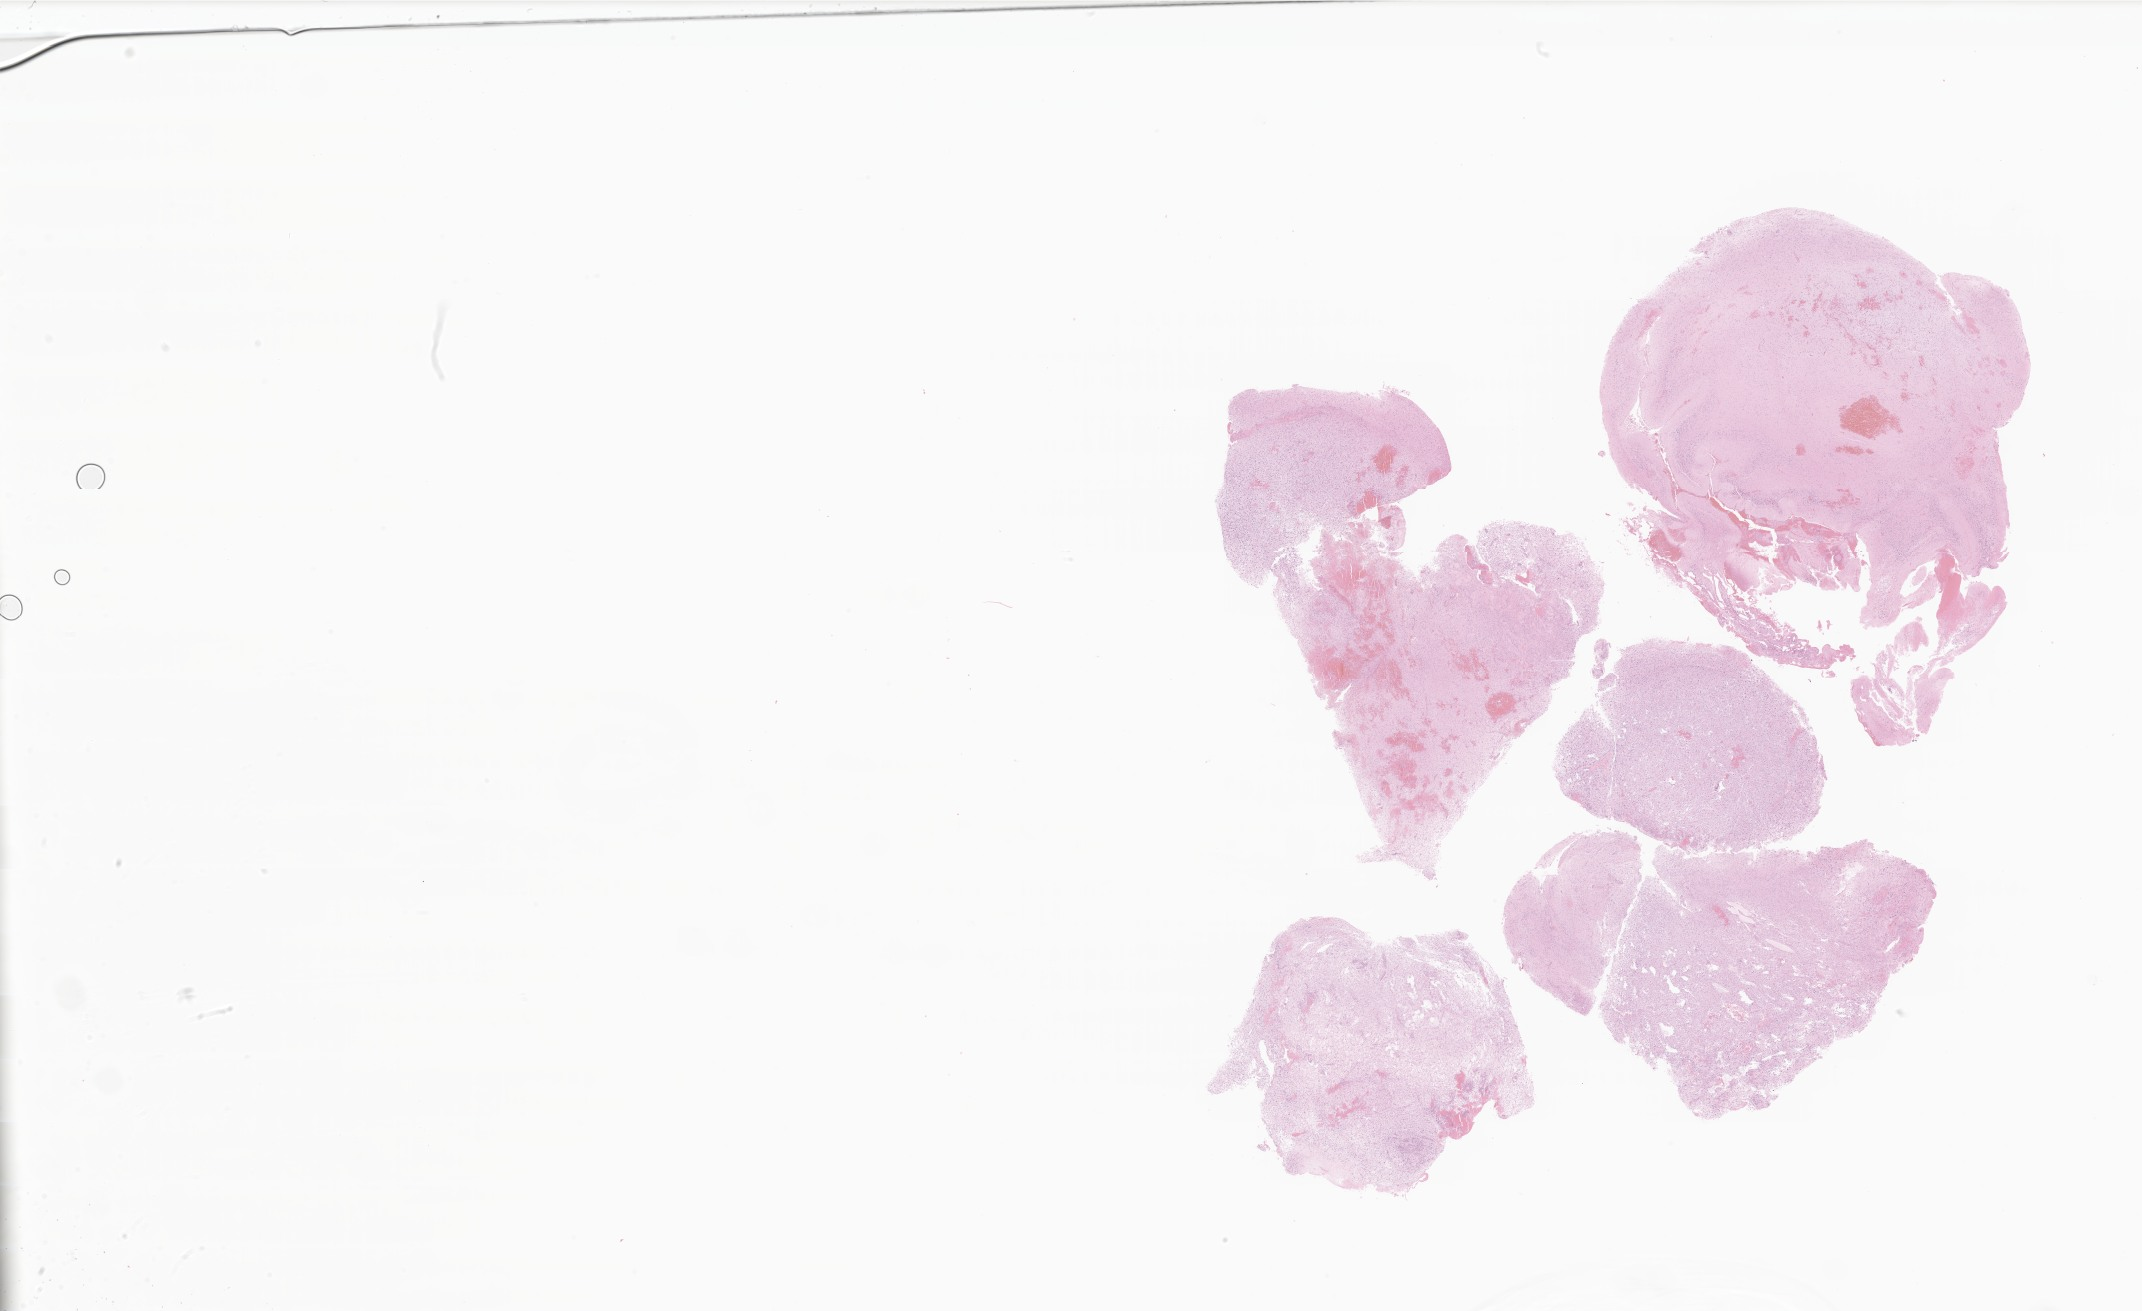
H&E whole-slide image of tumor tissue from the brain, whole scanned area (about 36.1 x 22.1 mm) shown as a low-resolution overview; formalin-fixed, paraffin-embedded (FFPE) tissue. Patient: male, age 113 months.
- recorded diagnosis: Pilocytic astrocytoma